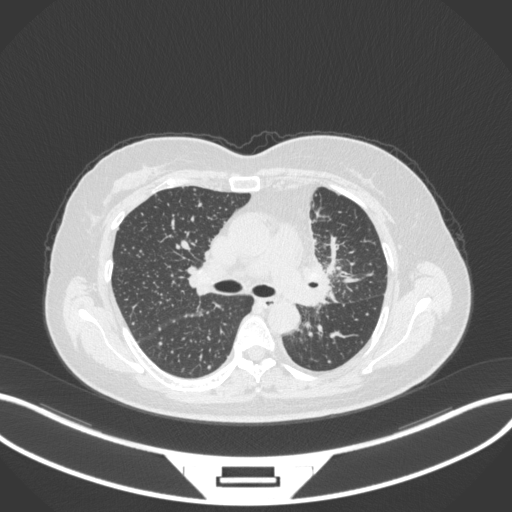
Chest CT, one axial slice. Slice 208 of 348 in the series (ordered by position). Reconstruction kernel B31f. Lung window (W 1500 / L -600 HU). 512 × 512 image matrix, field of view 400 × 400 mm. Patient: female, 49 years. Case-level facts recorded for this patient, not image findings: clinical TNM (as recorded): T1c N0 M1.
Outlined on this slice (bounding box drawn by a radiologist):
- lung tumour (recorded histology: adenocarcinoma): bounding box [x1, y1, x2, y2] px = [287, 251, 337, 314]